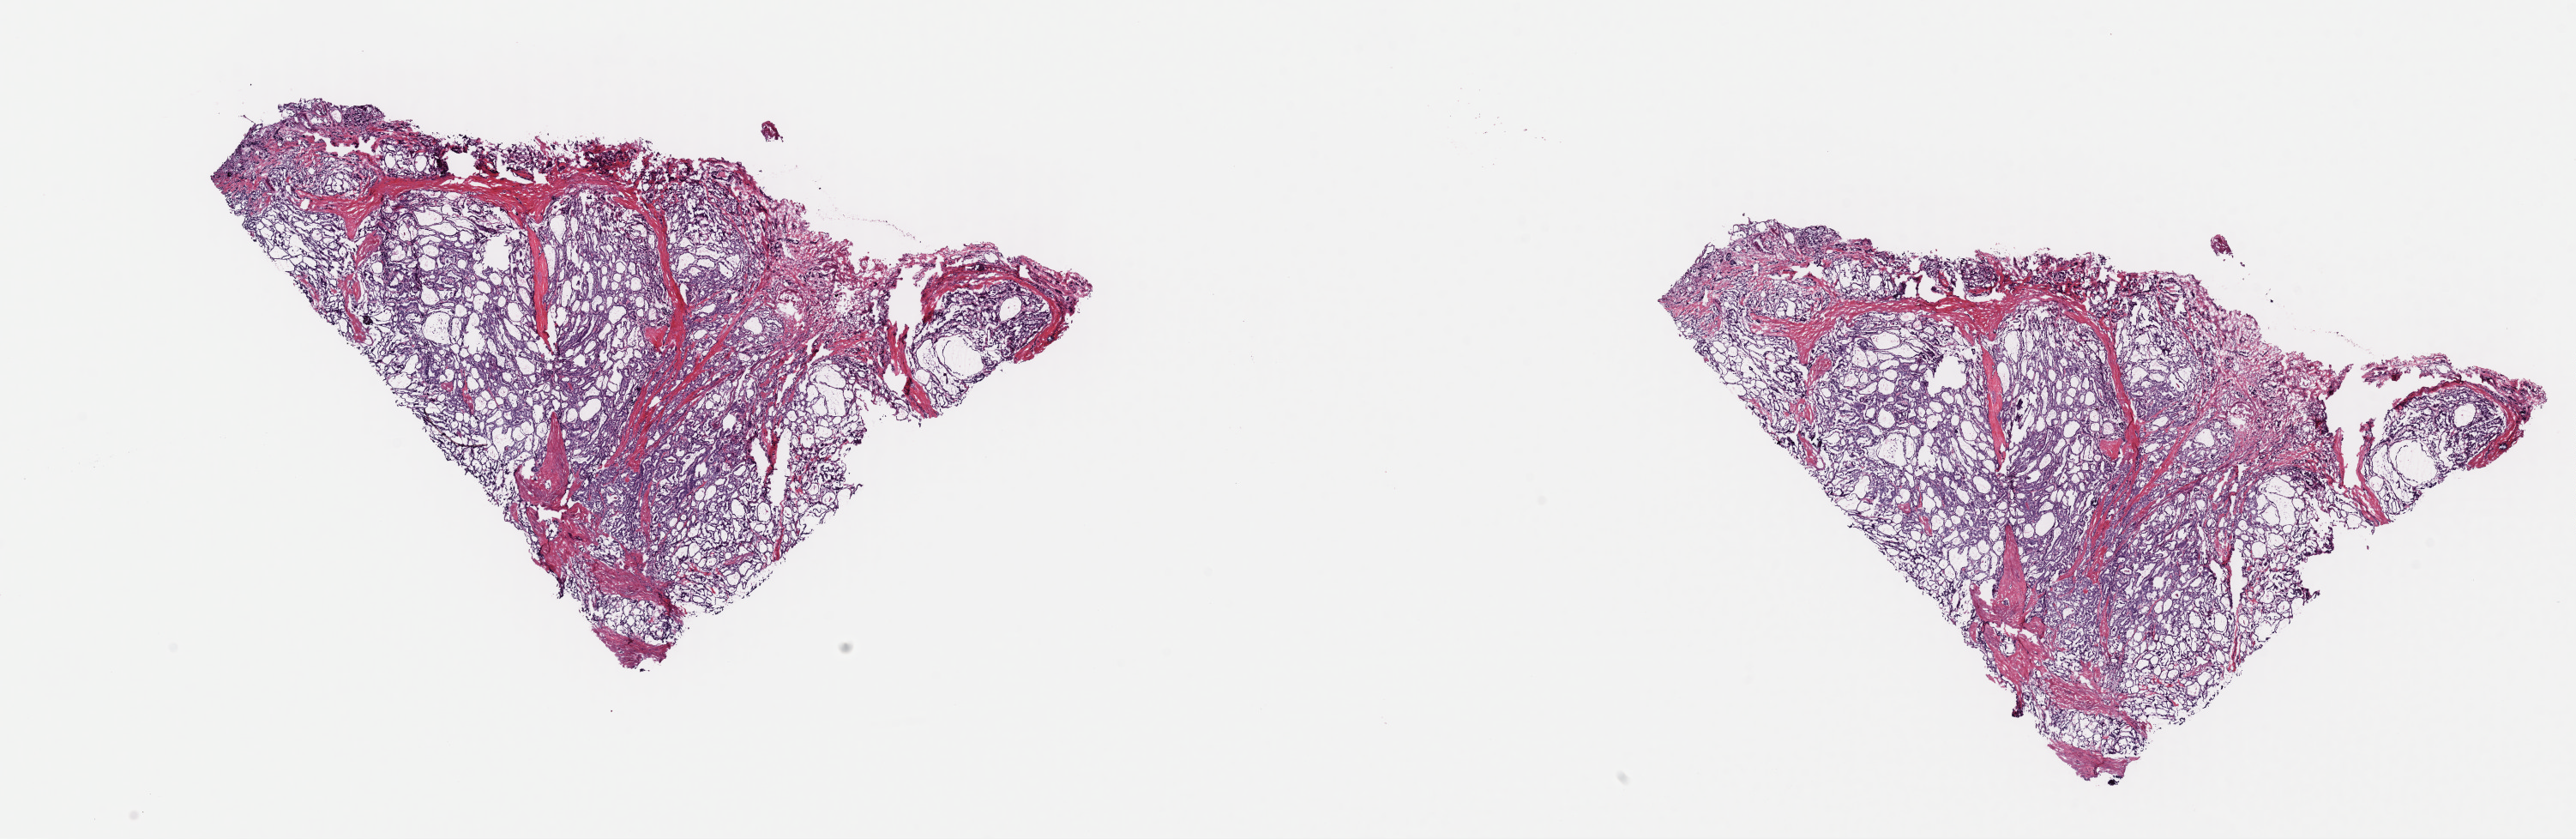
Whole-slide histology image, H&E-stained, shown as a low-resolution overview of the whole scanned area (about 23.7 x 7.7 mm). Frozen section. Sample: primary tumour, thyroid. Patient: female, age at initial diagnosis 52 years. Composition of this section per pathologist review: tumour cells 80%, tumour nuclei 85%.
Diagnosis: Papillary adenocarcinoma, NOS (thyroid gland).